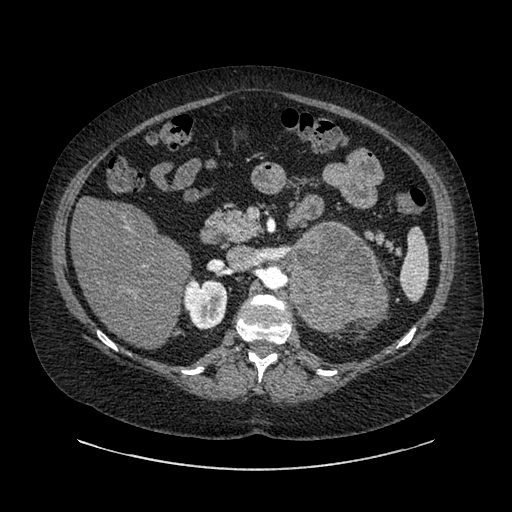
Contrast-enhanced abdominal CT, one axial slice. Position 543 of 769 along the scan axis. Reconstruction kernel SOFT. 120 kVp. Intravenous contrast given. Soft-tissue window (W 400 / L 40 HU). 0.62 mm slice thickness. 512 × 512 image matrix, field of view 460 × 460 mm. Female patient, age 61 years. Case-level facts recorded for this patient, not image findings: diagnosis: adrenocortical carcinoma; tumour side: left adrenal.
Structures marked on this image (semi-automatic segmentation, software-assisted and operator-edited):
- mass: box from (x=290, y=225) to (x=380, y=330) px